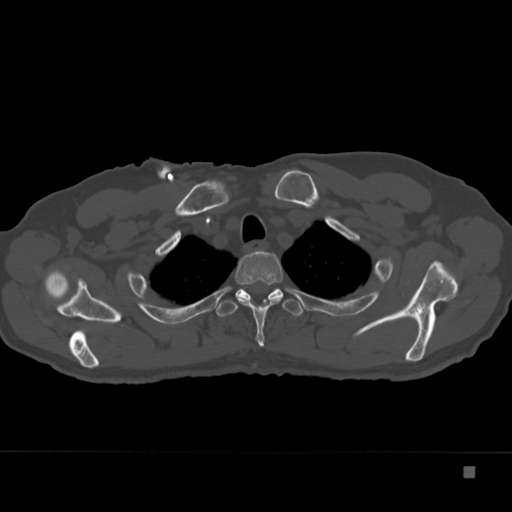
CT including the spine, one axial slice; slice 295 of 332 in the series (ordered by position); reconstruction kernel Br40s; 120 kVp; bone window (W 1800 / L 400 HU); 1.5 mm slice thickness; 512 × 512 image matrix. Patient: male, 72 years. From the clinical record (not read from this slice): primary cancer: skeletal.
Structures marked on this image (semi-automatic segmentation, software-assisted and operator-edited):
- T2 vertebra: bounding box (x1, y1, x2, y2) in pixels: (235, 251, 283, 347)
- T3 vertebra: (216, 288, 303, 317)